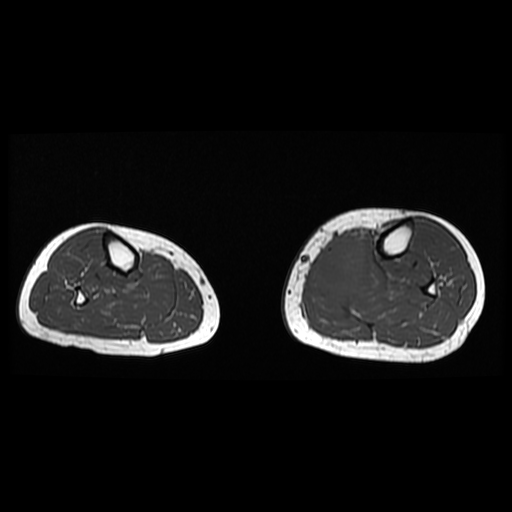
MRI of an extremity soft-tissue mass, one axial slice. Position 11 of 38 along the scan axis. 6 mm slice thickness. 512 × 512 image matrix, field of view 330 × 330 mm. Female patient. From the clinical record (not read from this slice): histological type: extraskeletal high grade osteogenic sarcoma; grade: high; site of the primary tumour: left calf.
Structures marked on this image (outlined manually by an expert reader):
- gross tumour volume (mass): bounding box <314,238,365,301> (left, top, right, bottom; pixels)